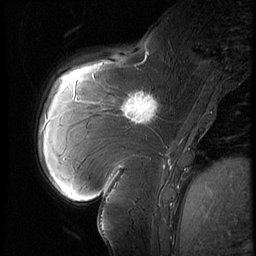
Breast MRI (dynamic contrast-enhanced), one sagittal slice. Position 20 of 60 along the scan axis. 3 images stored at this slice position (order not interpretable as contrast timing). 1.5 T. TE 4.2 ms, TR 9 ms. 2.5 mm slice thickness. 256 × 256 image matrix. Patient: female, 57 years. Case-level facts recorded for this patient, not image findings: setting: breast cancer imaged before/during neoadjuvant chemotherapy; receptor status: triple-negative.
Structures marked on this image (semi-automatically segmented with operator editing):
- analysis volume of interest (the breast-tissue region the enhancement analysis was run in; not a lesion): box from (x=114, y=83) to (x=170, y=131) px
- tumour enhancement mask (voxels above the 140 % enhancement threshold inside the analysis volume of interest): (x=120, y=93)–(x=159, y=124)